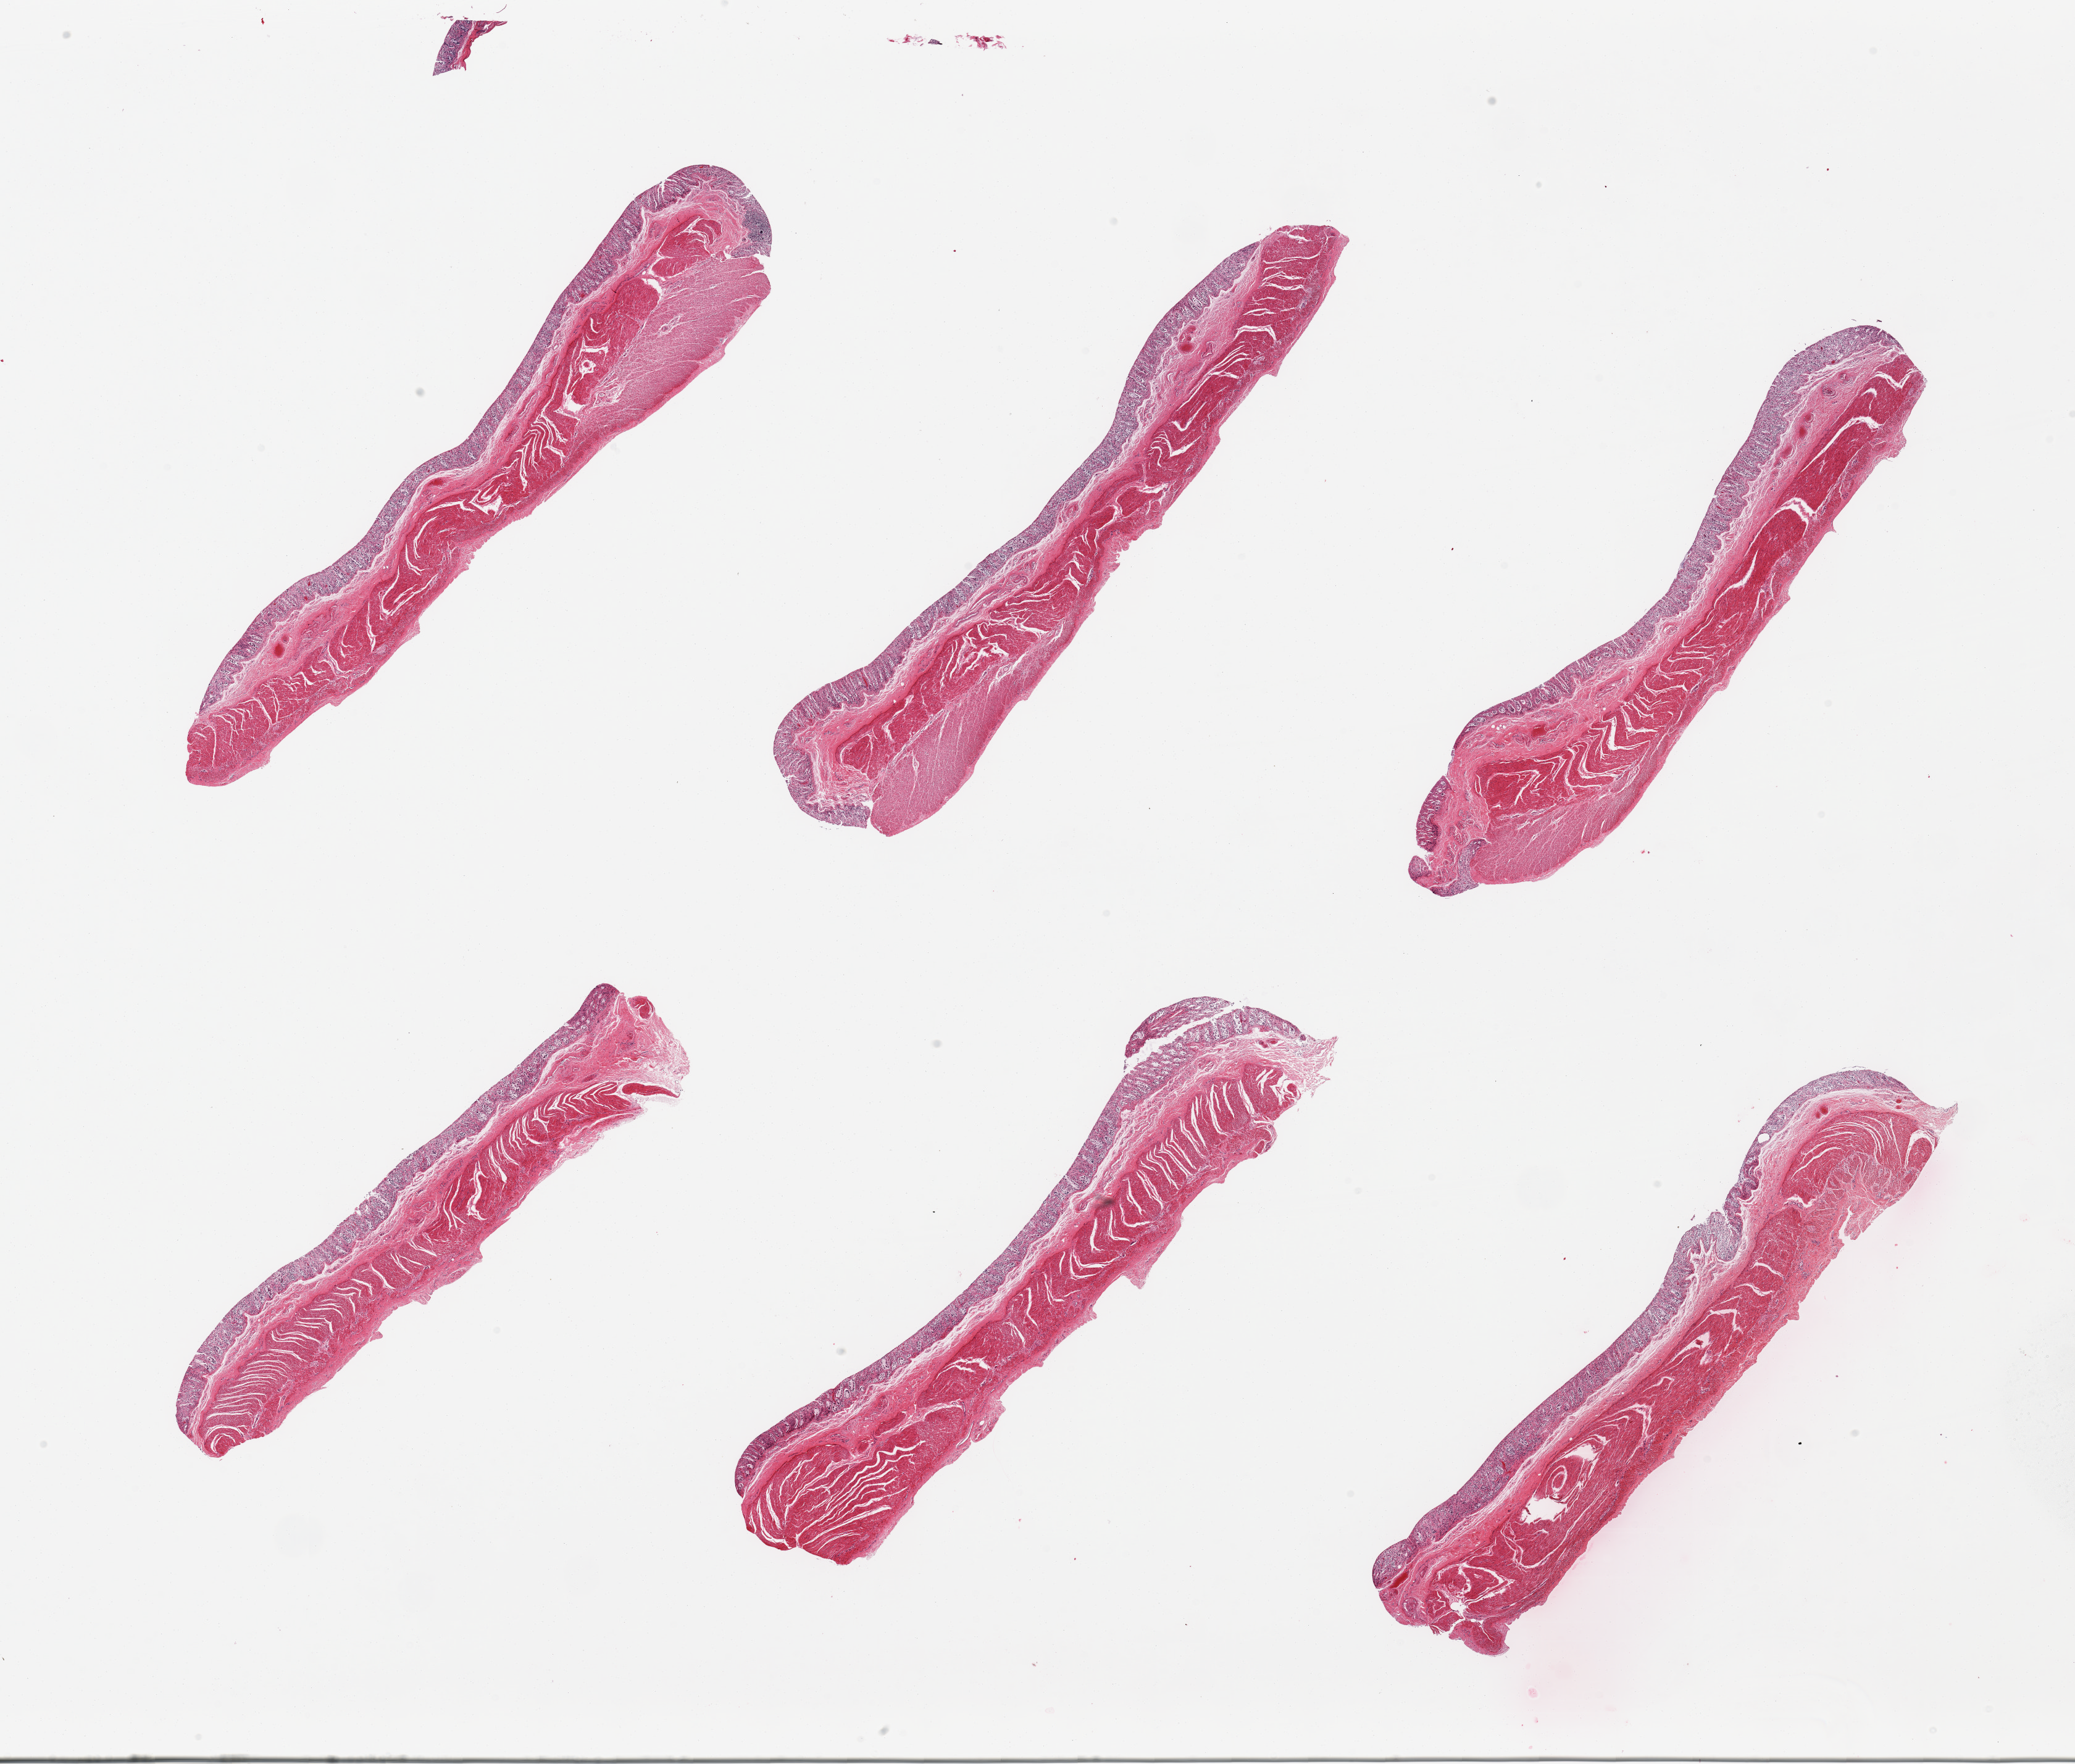
Digitized haematoxylin and eosin-stained section, brightfield, a low-resolution overview of the entire scanned area, about 26.6 x 22.6 mm (from a 20x scan), PAXgene-fixed, paraffin-embedded tissue, sampled site (target tissue): transverse colon, tissue donor sample. Male donor.
Reviewer comment on this tissue sample: 6 pieces, glandular mucosa completely autolyzed, mucosa up to~0.3mm.